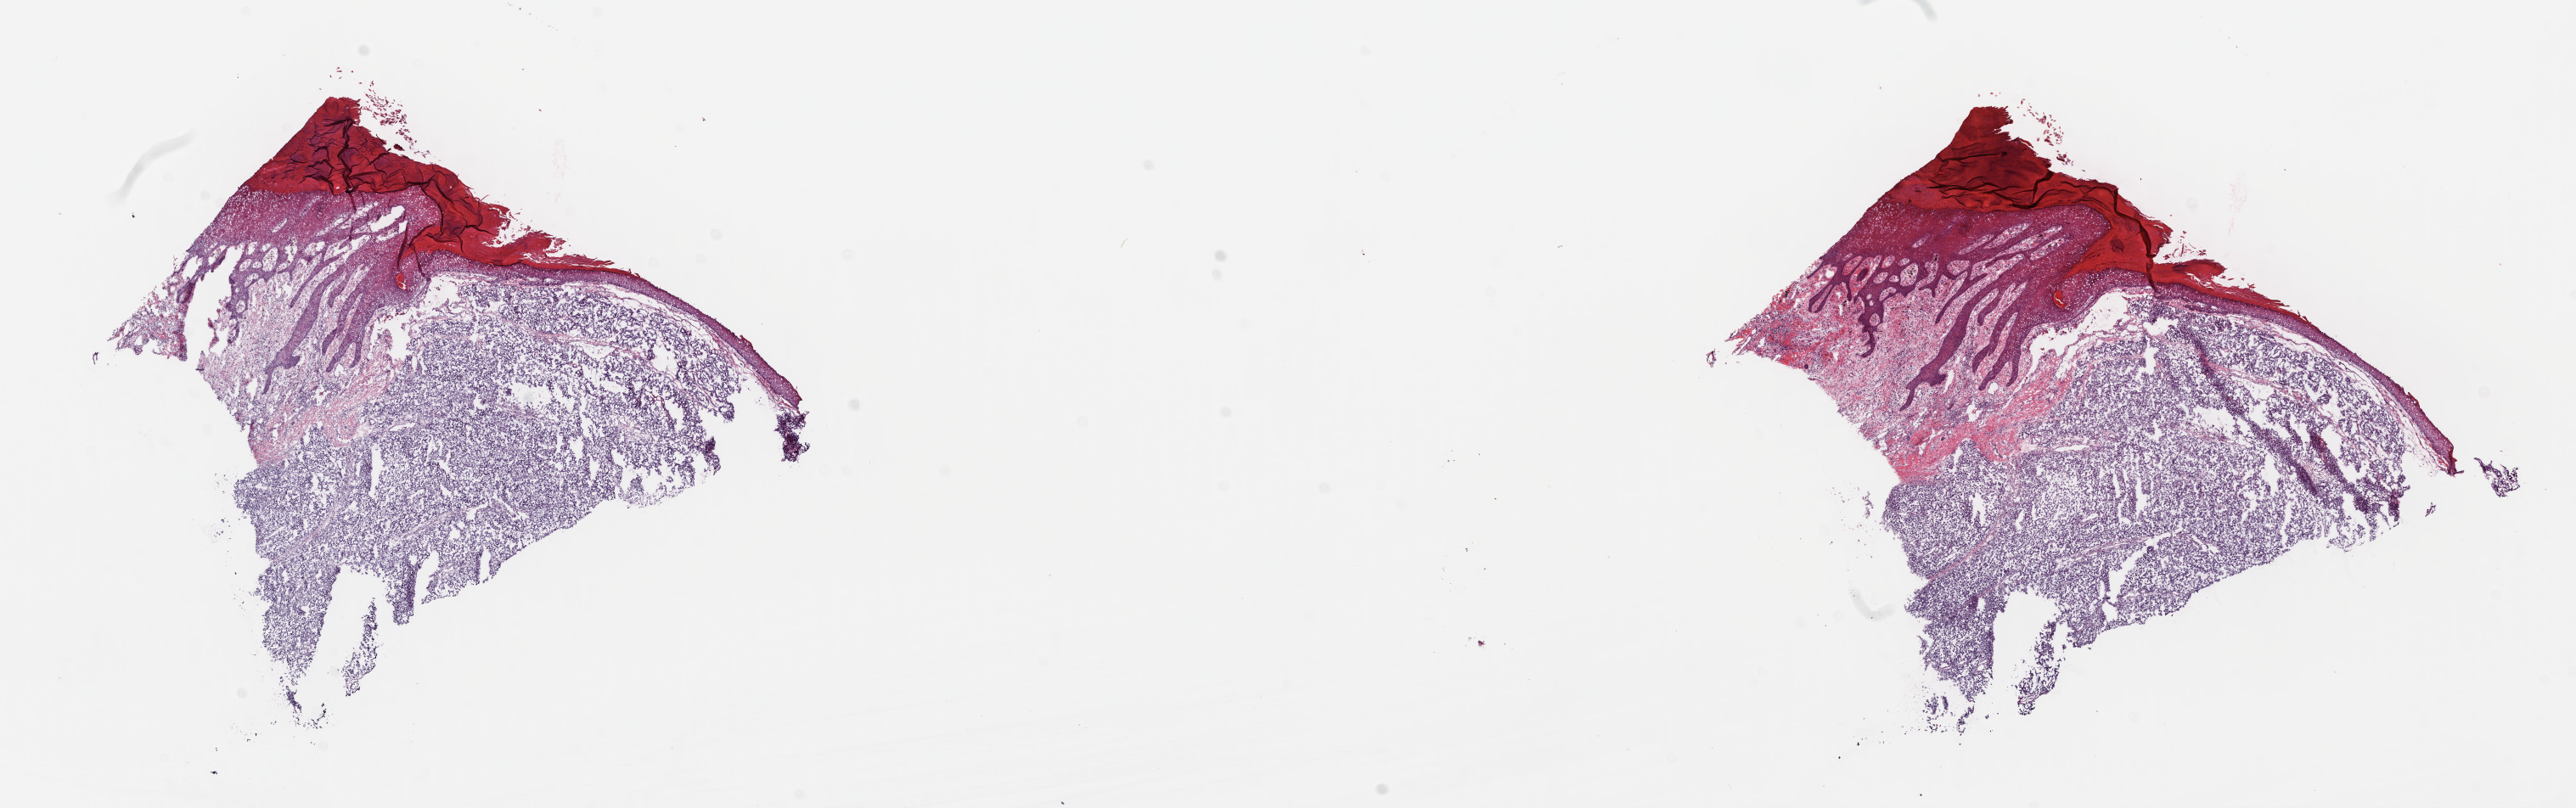
Digitized H&E tissue section (whole slide), low-resolution overview of the scanned area, about 23.8 x 7.5 mm (from a 40x scan). Frozen section. Primary tumour sample from the skin. Patient: male, age at initial diagnosis 56 years. Pathologist review of this section (percent, as recorded): tumour cells 80%, tumour nuclei 75%, normal cells 20%, stromal cells 0%, necrosis 0%. Inflammatory infiltration, as recorded: lymphocyte infiltration 3%, monocyte infiltration 1%, neutrophil infiltration 0%.
Diagnosis: Malignant melanoma, NOS.